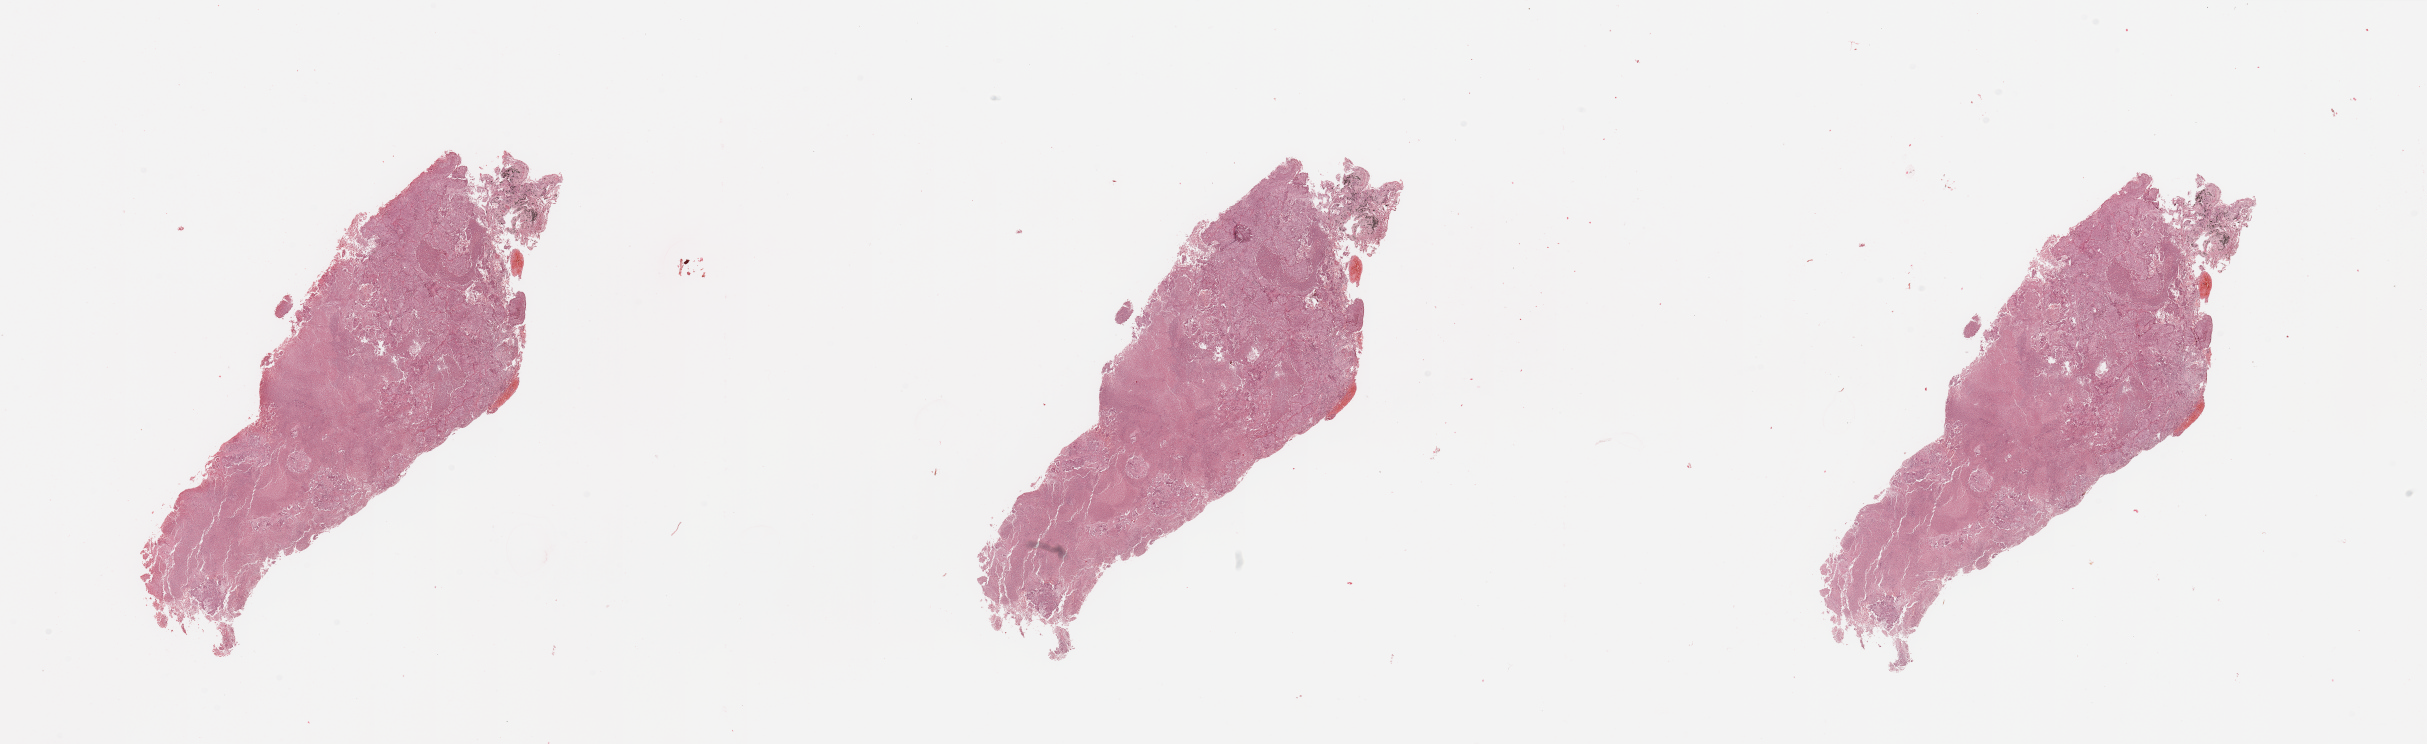
Hematoxylin and eosin (H&E) stained whole-slide image, shown as a low-resolution overview of the whole scanned area (about 38.4 x 11.8 mm). Tumour tissue sample, lung. 71-year-old male patient.
Patient diagnosis (cohort enrolment): squamous cell carcinoma (lung).